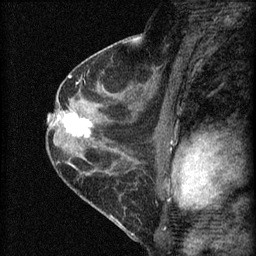
Breast MRI (dynamic contrast-enhanced), one sagittal slice. Slice 36 of 60 in the series (ordered by position). Dynamic contrast-enhanced series, image 2 of 4 at this slice position (ordered by acquisition). 1.5 T. TE 4.2 ms, TR 8.2 ms. 256 × 256 image matrix, field of view 180 × 180 mm. Patient: female, 45 years.
Annotated regions visible in this slice (semi-automatic segmentation, software-assisted and operator-edited):
- analysis volume of interest (the breast-tissue region the enhancement analysis was run in; not a lesion): bounding box <58,107,98,147> (left, top, right, bottom; pixels)
- tumour enhancement mask (voxels above the 70 % enhancement threshold inside the analysis volume of interest): <64,113,92,137>